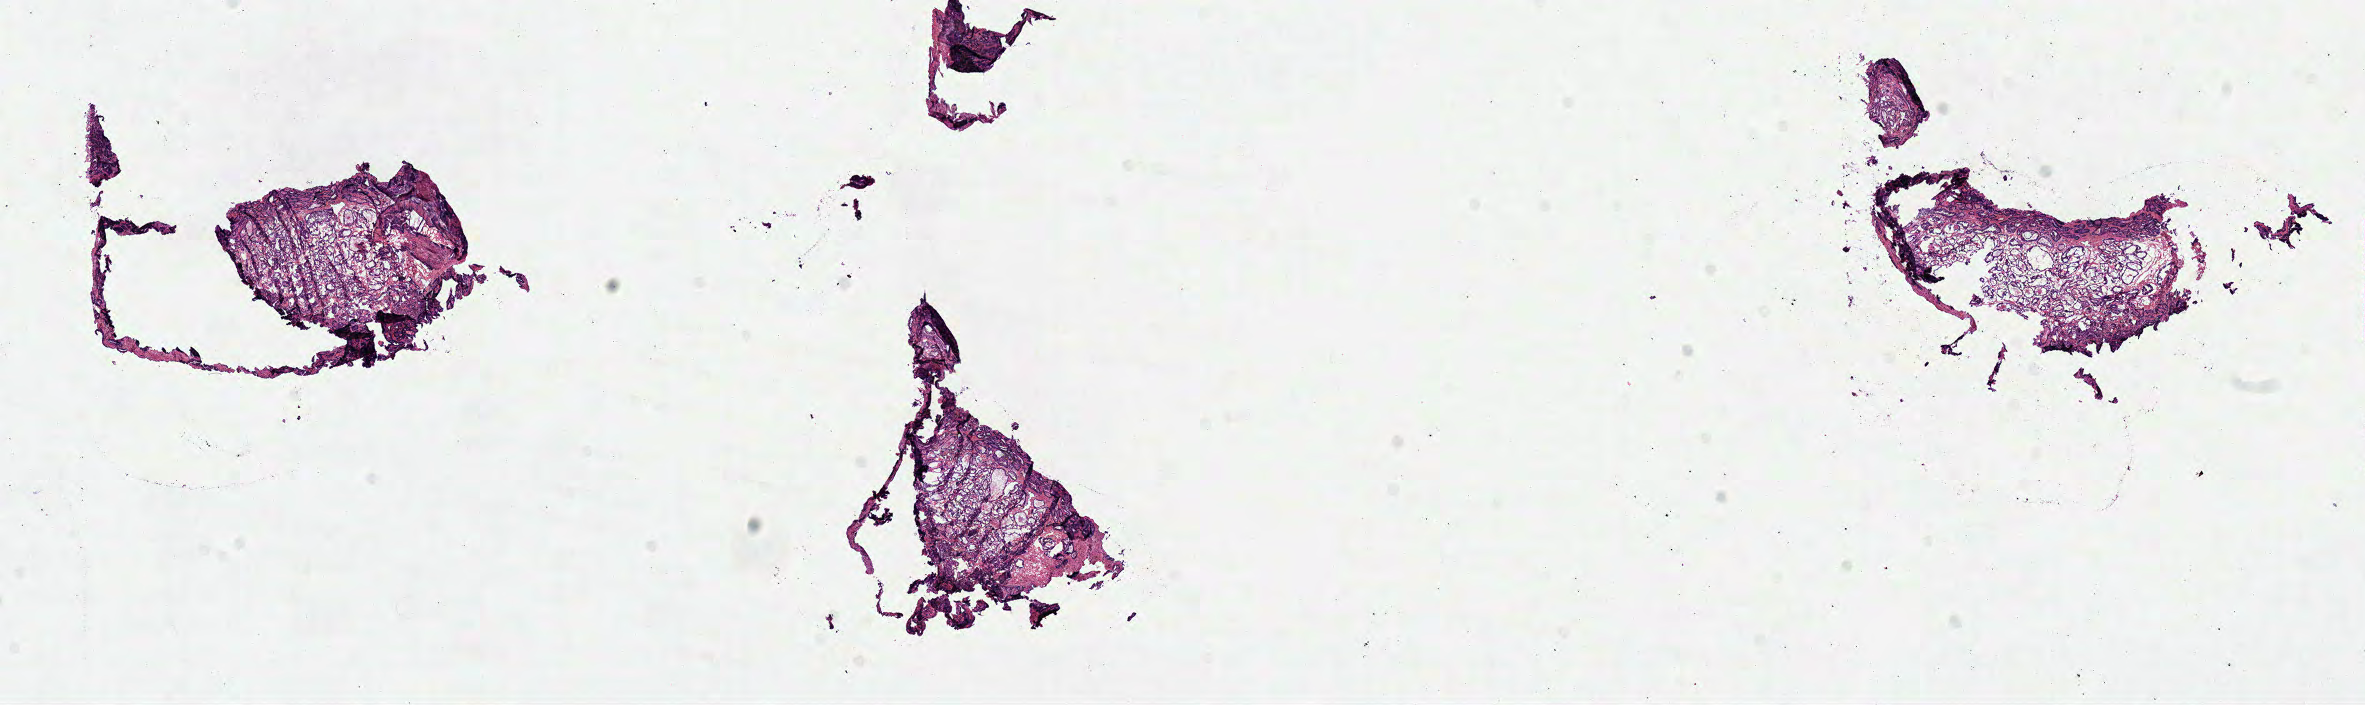
Whole-slide histology image, Hematoxylin and eosin (H&E) stained — a low-resolution overview of the entire scanned area, about 18.6 x 5.5 mm (from a 40x scan). Frozen section from the top of the tissue portion. Prostate, primary tumour sample. Patient: male, age at initial diagnosis 55 years. Gleason score: 7 (3+4). Pathologist review of this section (percent, as recorded): tumour cells 70%, tumour nuclei 80%, normal cells 5%, stromal cells 25%, necrosis 0%. Infiltration values recorded for this section: lymphocyte infiltration 0%, monocyte infiltration 0%, neutrophil infiltration 0%.
* histologic diagnosis: Acinar cell carcinoma (prostate gland)
* laterality: right